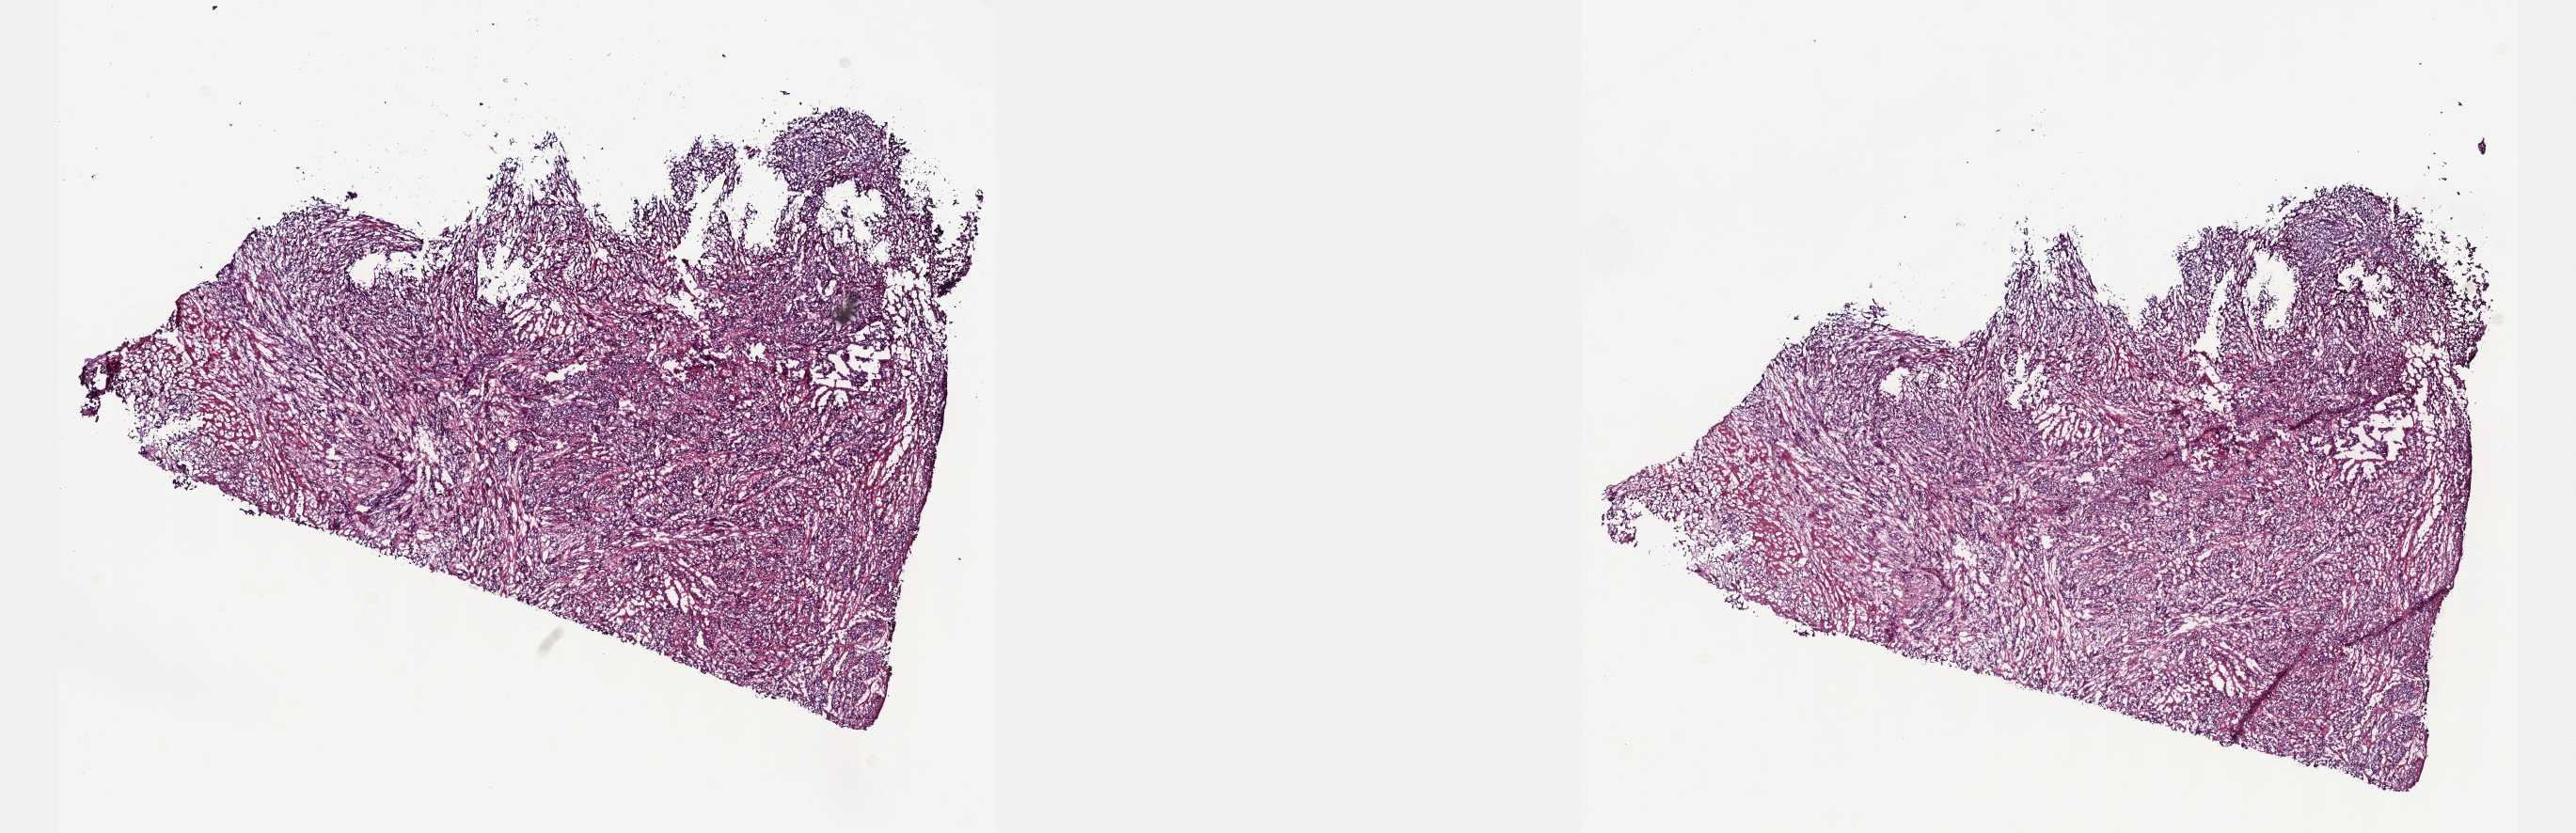
H&E-stained whole-slide image, low-resolution overview of the scanned area, about 22.1 x 7.2 mm; frozen section from the top of the tissue portion; sample: primary tumour, bladder. Patient: male, age at initial diagnosis 63 years. Histologic grade: high grade. Composition of this section per pathologist review: tumour cells 100%, tumour nuclei 75%, normal cells 0%, stromal cells 0%, necrosis 0%. Inflammatory infiltration, as recorded: lymphocyte infiltration 3%, monocyte infiltration 0%, neutrophil infiltration 0%.
- diagnosis: Transitional cell carcinoma
- AJCC pathologic stage: IV (6th edition)